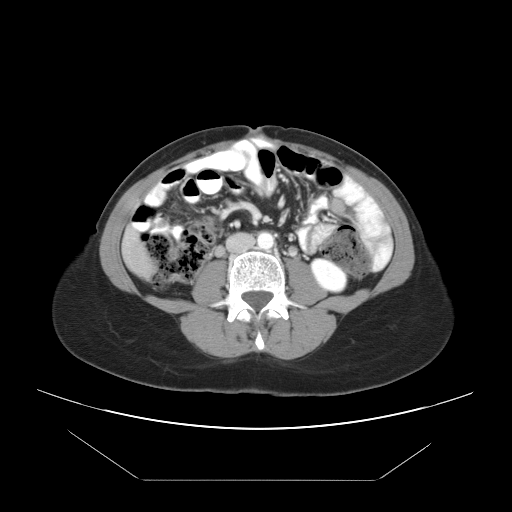
Contrast-enhanced abdominal CT, one axial slice. Slice 7 of 45 in the series (ordered by position). Intravenous contrast given. Soft-tissue window (W 400 / L 40 HU). 5 mm slice thickness. 512 × 512 image matrix, field of view 405 × 405 mm. Female patient, age 52 years. Case-level facts recorded for this patient, not image findings: diagnosis: colorectal cancer liver metastases, imaged before liver resection; multiple liver metastases: yes; largest metastasis: 2.5 cm; disease in both lobes: no.
Annotated regions visible in this slice (expert manual segmentation):
- liver: bounding box <124,231,153,276> (left, top, right, bottom; pixels)
- planned liver remnant (the part of the liver to remain after resection): <124,231,148,264>